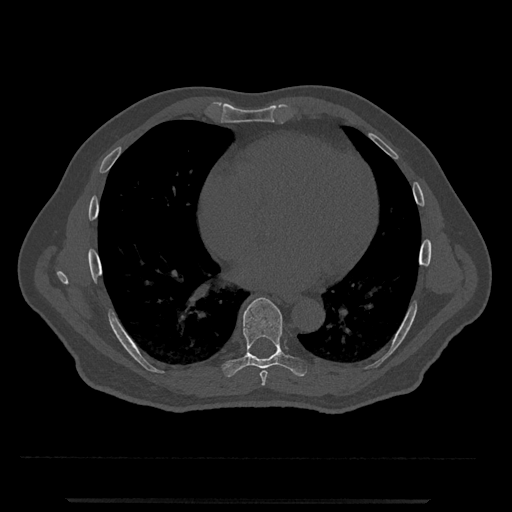
CT including the spine, one axial slice; slice 634 of 797 in the series (ordered by position); 120 kVp; bone window (W 1800 / L 400 HU); 0.5 mm slice thickness; 512 × 512 image matrix. Male patient, age 63 years. Case-level facts recorded for this patient, not image findings: primary cancer: prostate.
Annotated regions visible in this slice (semi-automatically segmented with operator editing):
- T7 vertebra: box from (x=260, y=371) to (x=268, y=386) px
- T8 vertebra: (x=222, y=297)–(x=307, y=377)